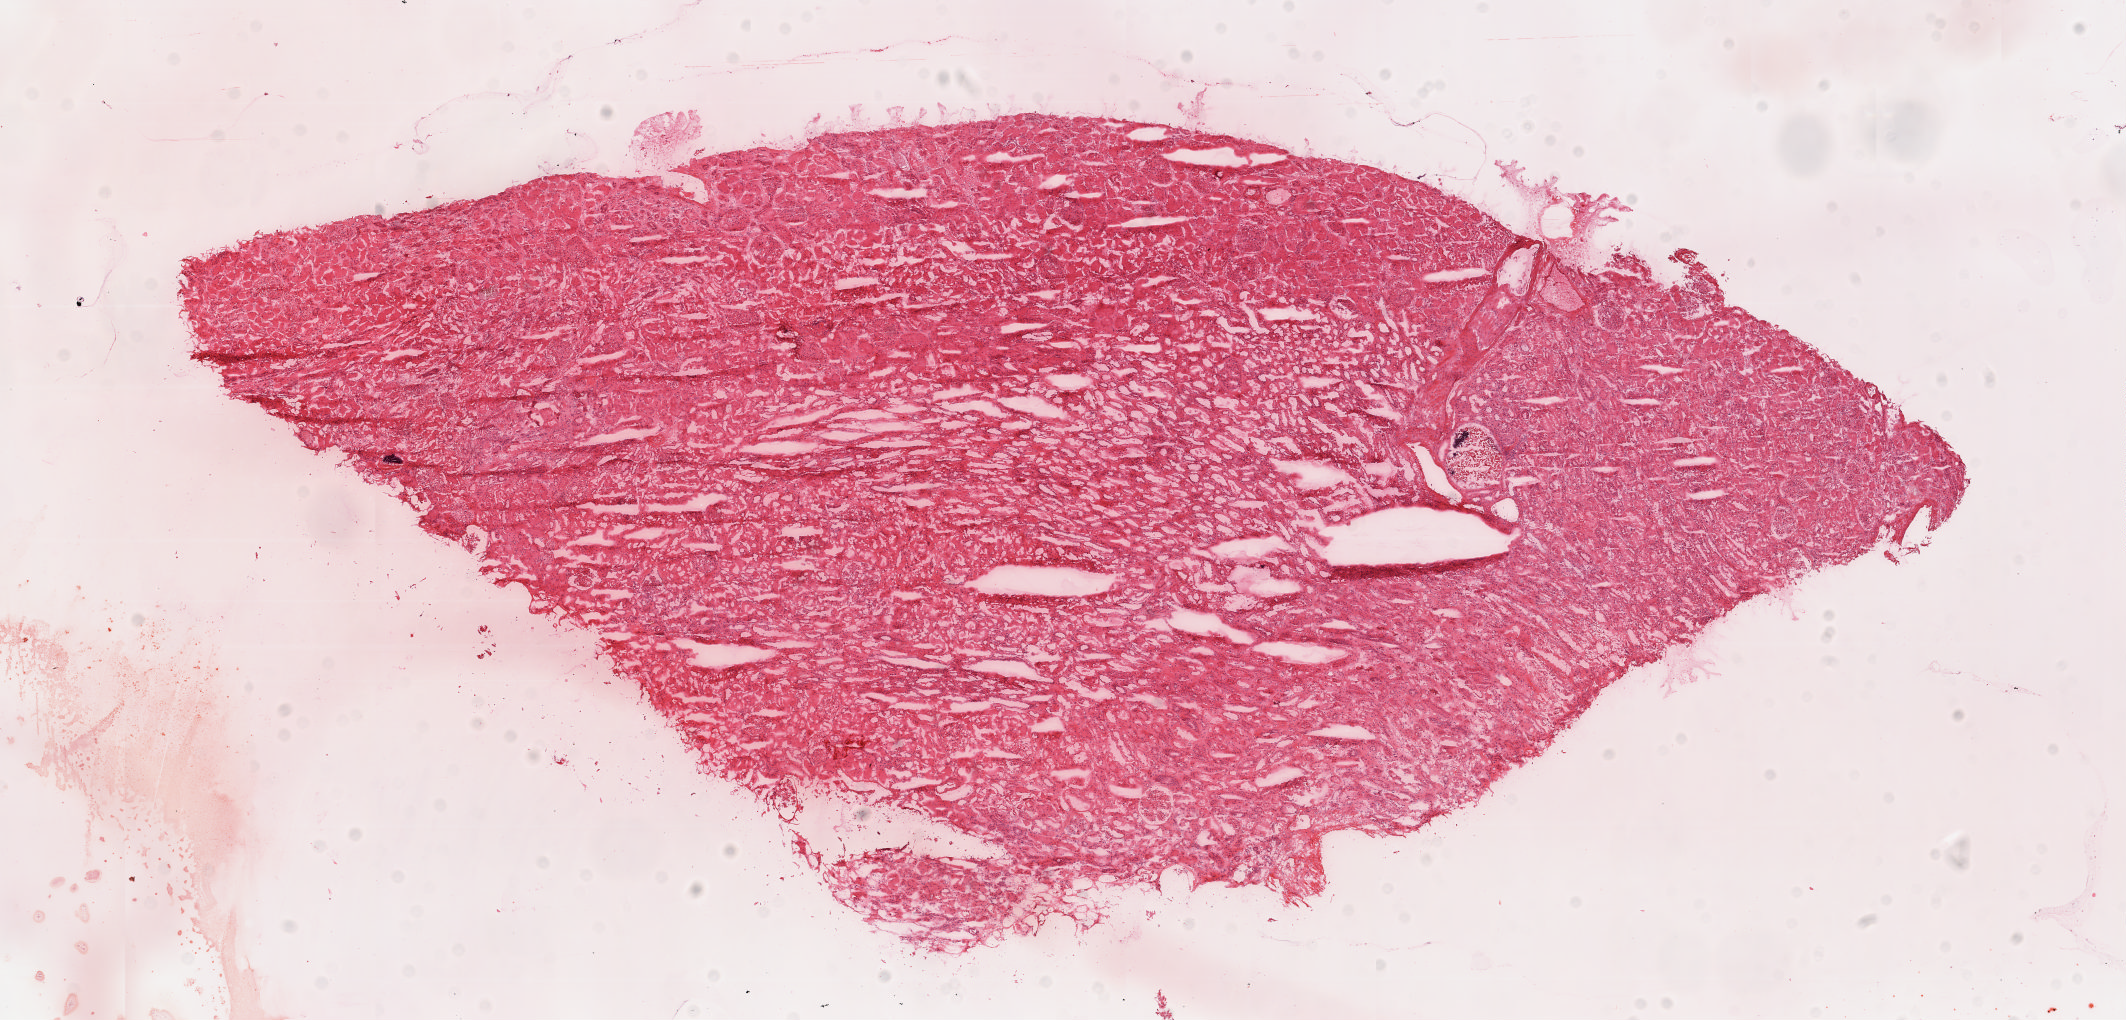
Digitized H&E-stained tissue section (whole slide) — a low-resolution overview of the entire scanned area, about 16.9 x 8.1 mm. Frozen section. Solid tissue normal (non-tumour tissue) sample from the kidney. Male patient; age at initial diagnosis 74 years.
This section: solid tissue normal (non-tumour) sample from the same patient. Patient diagnosis: Clear cell adenocarcinoma, NOS.